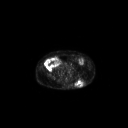
FDG PET of an extremity soft-tissue mass (from a PET/CT study), one axial slice. Position 92 of 267 along the scan axis. 3.27 mm slice thickness. 128 × 128 image matrix, field of view 700 × 700 mm. Male patient, age 69 years. Case-level facts recorded for this patient, not image findings: histological type: leiomyosarcoma; grade: intermediate; site of the primary tumour: left pelvis.
Outlined on this slice (expert contour drawn on MRI and transferred to this co-registered scan by the dataset authors):
- gross tumour volume (mass): box from (x=75, y=79) to (x=85, y=87) px